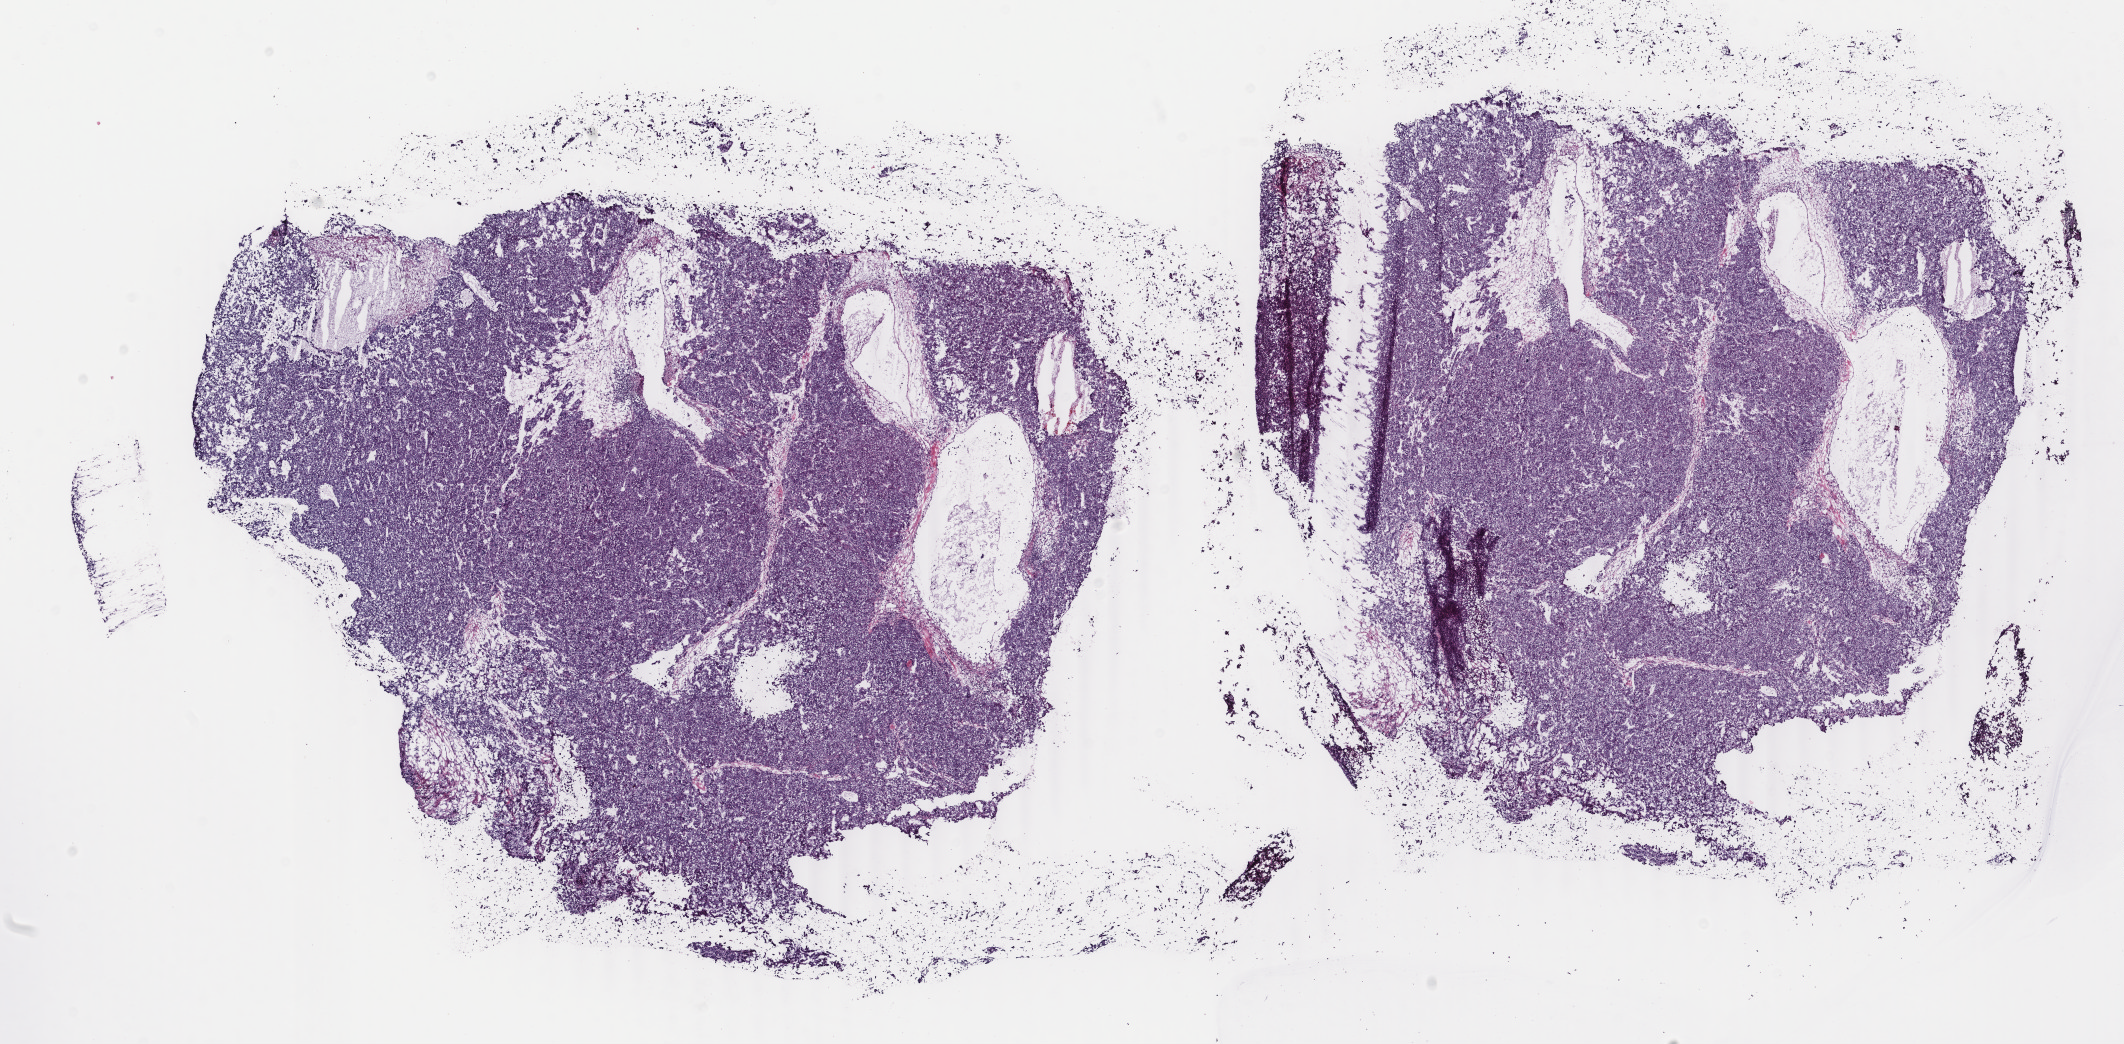
H&E-stained whole-slide image — low-resolution overview of the scanned area, about 16.9 x 8.3 mm (slide scanned at 40x), frozen section, liver, primary tumour sample. Male patient; age at initial diagnosis 76 years. Composition of this section per pathologist review: tumour cells 85%, tumour nuclei 85%.
Histologic diagnosis: Hepatocellular carcinoma, NOS.